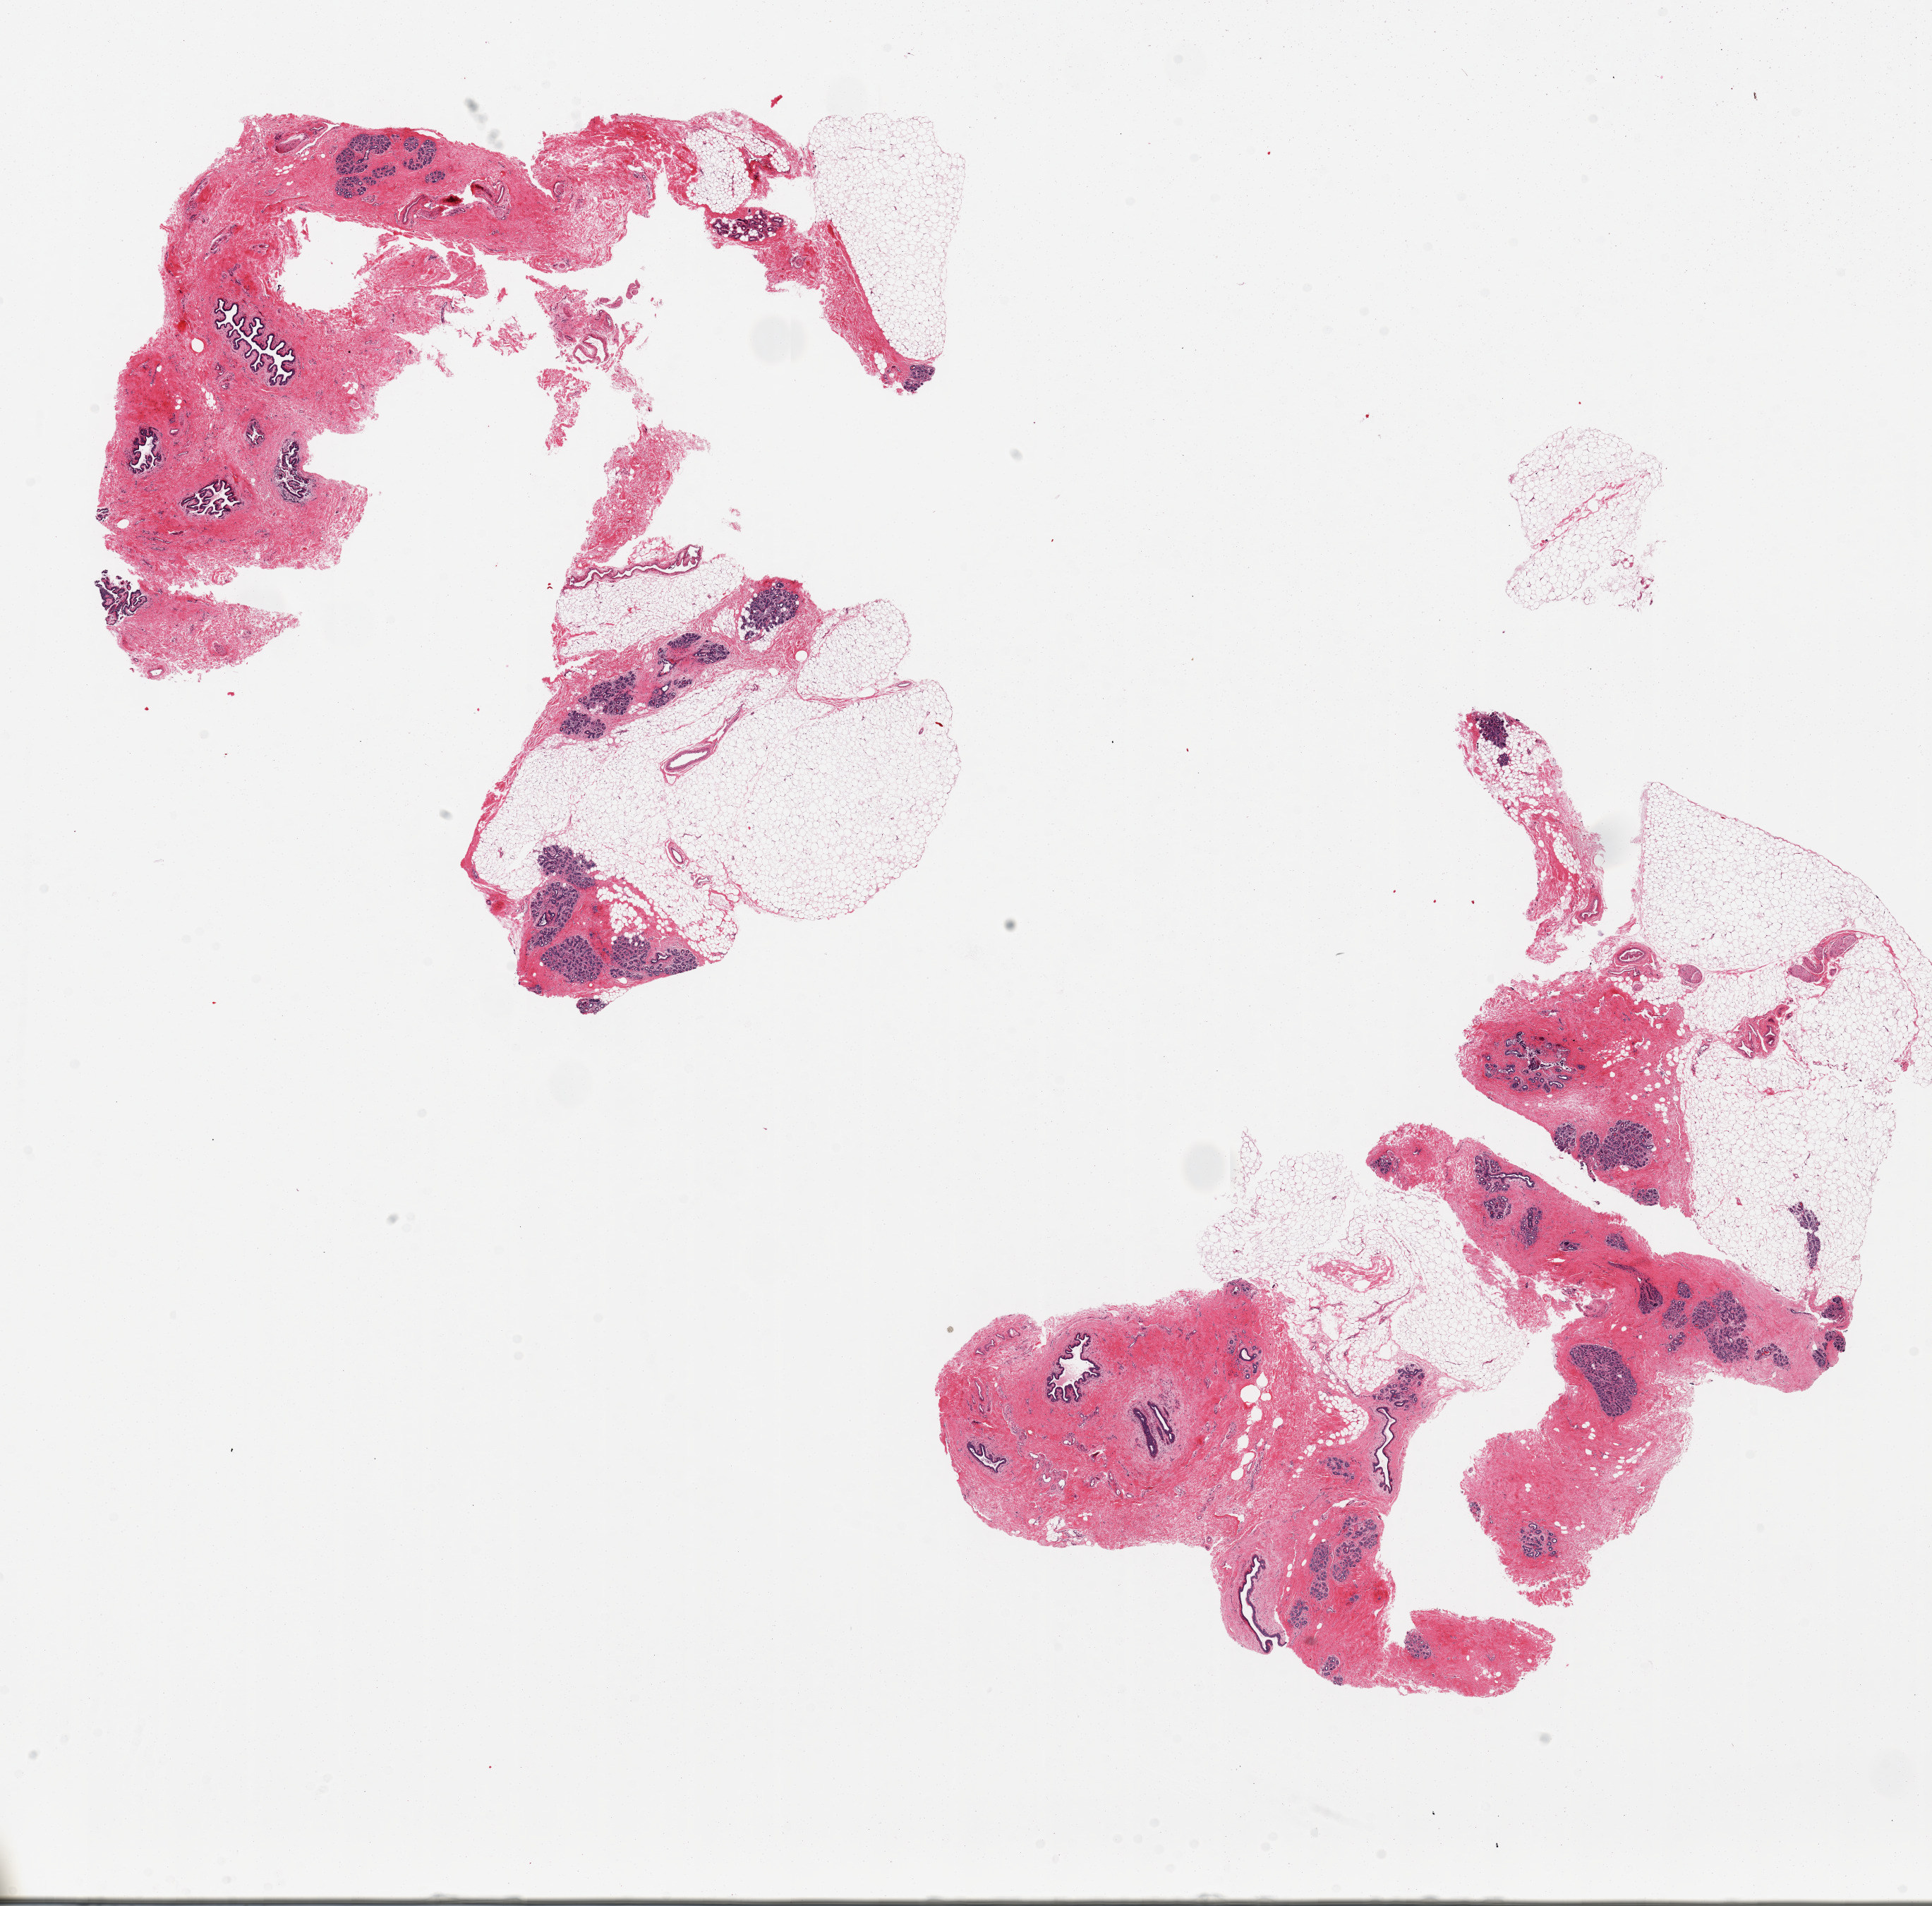
Whole-slide image, hematoxylin and eosin (H&E) stain — a low-resolution overview of the entire scanned area, about 21.7 x 21.4 mm (slide scanned at 20x). PAXgene-fixed, paraffin-embedded tissue. Section of breast (target tissue). Tissue donor sample. Donor sex: female.
Pathologist's review note for this sample: 2 pieces, TDLUs well seen, ~10-15% of sections, rest fibro-fatty tissue.